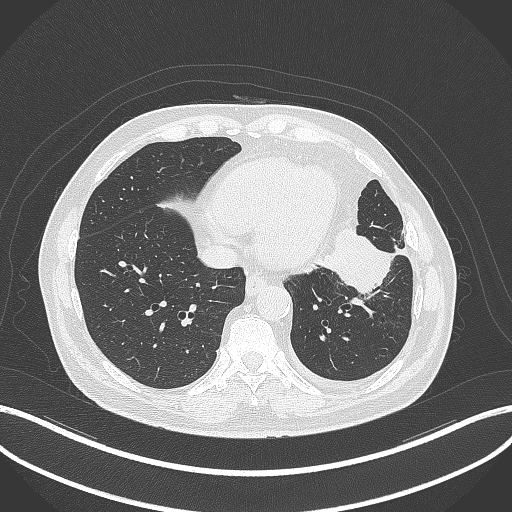
Chest CT, one axial slice; position 108 of 230 along the scan axis; lung window (W 1500 / L -600 HU); 512 × 512 image matrix, field of view 400 × 400 mm. Male patient, age 68 years. From the clinical record (not read from this slice): clinical TNM (as recorded): T2b N0 M0.
Structures marked on this image (rectangle marked by the reading radiologist):
- lung tumour (recorded histology: squamous cell carcinoma): bounding box [x1, y1, x2, y2] px = [319, 225, 398, 295]